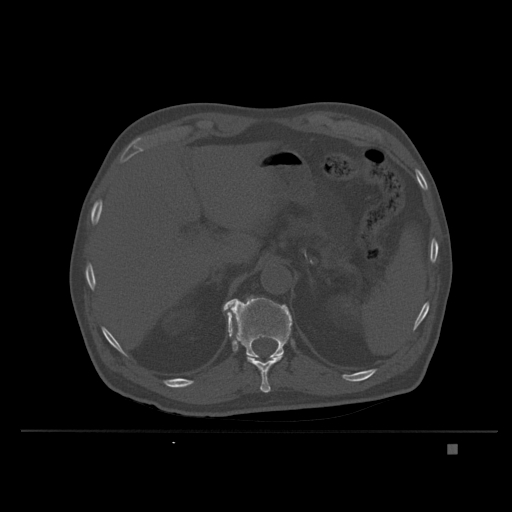
CT including the spine, one axial slice. Position 167 of 435 along the scan axis. Bone window (W 1800 / L 400 HU). 1.5 mm slice thickness. 512 × 512 image matrix. Patient: male, 73 years. Case-level facts recorded for this patient, not image findings: primary cancer: skin.
Annotated regions visible in this slice (semi-automatic segmentation, software-assisted and operator-edited):
- T11 vertebra: bounding box [x1, y1, x2, y2] px = [228, 314, 284, 393]
- T12 vertebra: [223, 296, 293, 358]